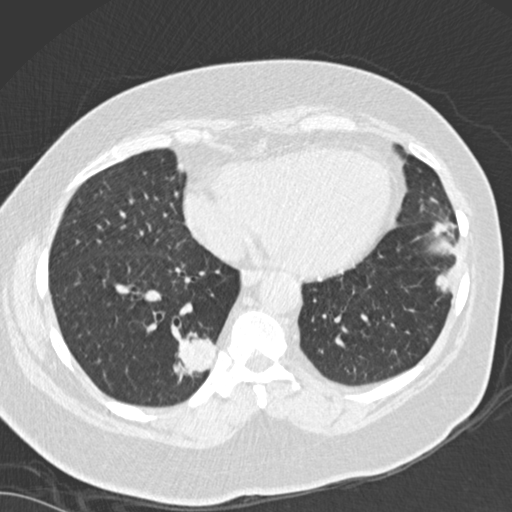
Chest CT (low-dose screening protocol), one axial image, baseline annual screen, lung window (W 1500 / L -600 HU), 2 mm slice thickness, slice 108 of 162 in the series. Female, age 66 years at enrolment. Current smoker at enrolment.
Expert-annotated lung lesion, bounding box [x1, y1, x2, y2] px = [144, 314, 235, 408]. The screening reader recorded 3 non-calcified nodules or masses ≥4 mm on this exam; which of them this box marks is not recorded. Official screen result: positive, change unspecified: nodule(s) >= 4 mm or enlarging nodule(s), mass(es), or other non-specific abnormalities suspicious for lung cancer. Later outcome: lung cancer diagnosed 67 days after this screen — adenocarcinoma, NOS, right lower lobe, well differentiated (G1), stage IB (AJCC 6th edition), 55 mm at pathology.